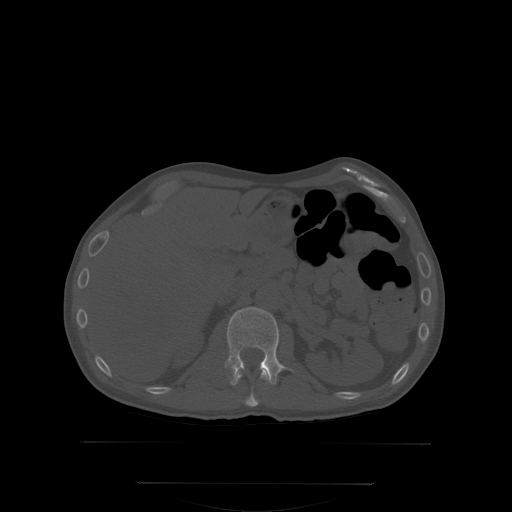
CT including the spine, one axial slice; position 157 of 350 along the scan axis; bone window (W 1800 / L 400 HU); 2.5 mm slice thickness; 512 × 512 image matrix. Patient: male, 58 years. Case-level facts recorded for this patient, not image findings: primary cancer: prostate; vertebrae with lytic lesions (as recorded): L1.
Annotated regions visible in this slice (semi-automatic segmentation, software-assisted and operator-edited):
- L1 vertebra: bounding box (x1, y1, x2, y2) in pixels: (227, 307, 292, 384)
- T12 vertebra: (238, 367, 268, 406)